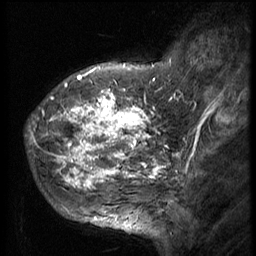
Breast MRI (dynamic contrast-enhanced), one sagittal slice; slice 15 of 56 in the series (ordered by position); 3 images stored at this slice position (order not interpretable as contrast timing); 1.5 T; TE 4.2 ms, TR 9 ms; 2.5 mm slice thickness; 256 × 256 image matrix, field of view 180 × 180 mm. Female patient, age 49 years. From the clinical record (not read from this slice): setting: breast cancer imaged before/during neoadjuvant chemotherapy; receptor status: HER2-positive.
Structures marked on this image (semi-automatic segmentation, software-assisted and operator-edited):
- analysis volume of interest (the breast-tissue region the enhancement analysis was run in; not a lesion): bounding box (x1, y1, x2, y2) in pixels: (37, 85, 154, 207)
- tumour enhancement mask (voxels above the 140 % enhancement threshold inside the analysis volume of interest): (42, 85, 154, 192)